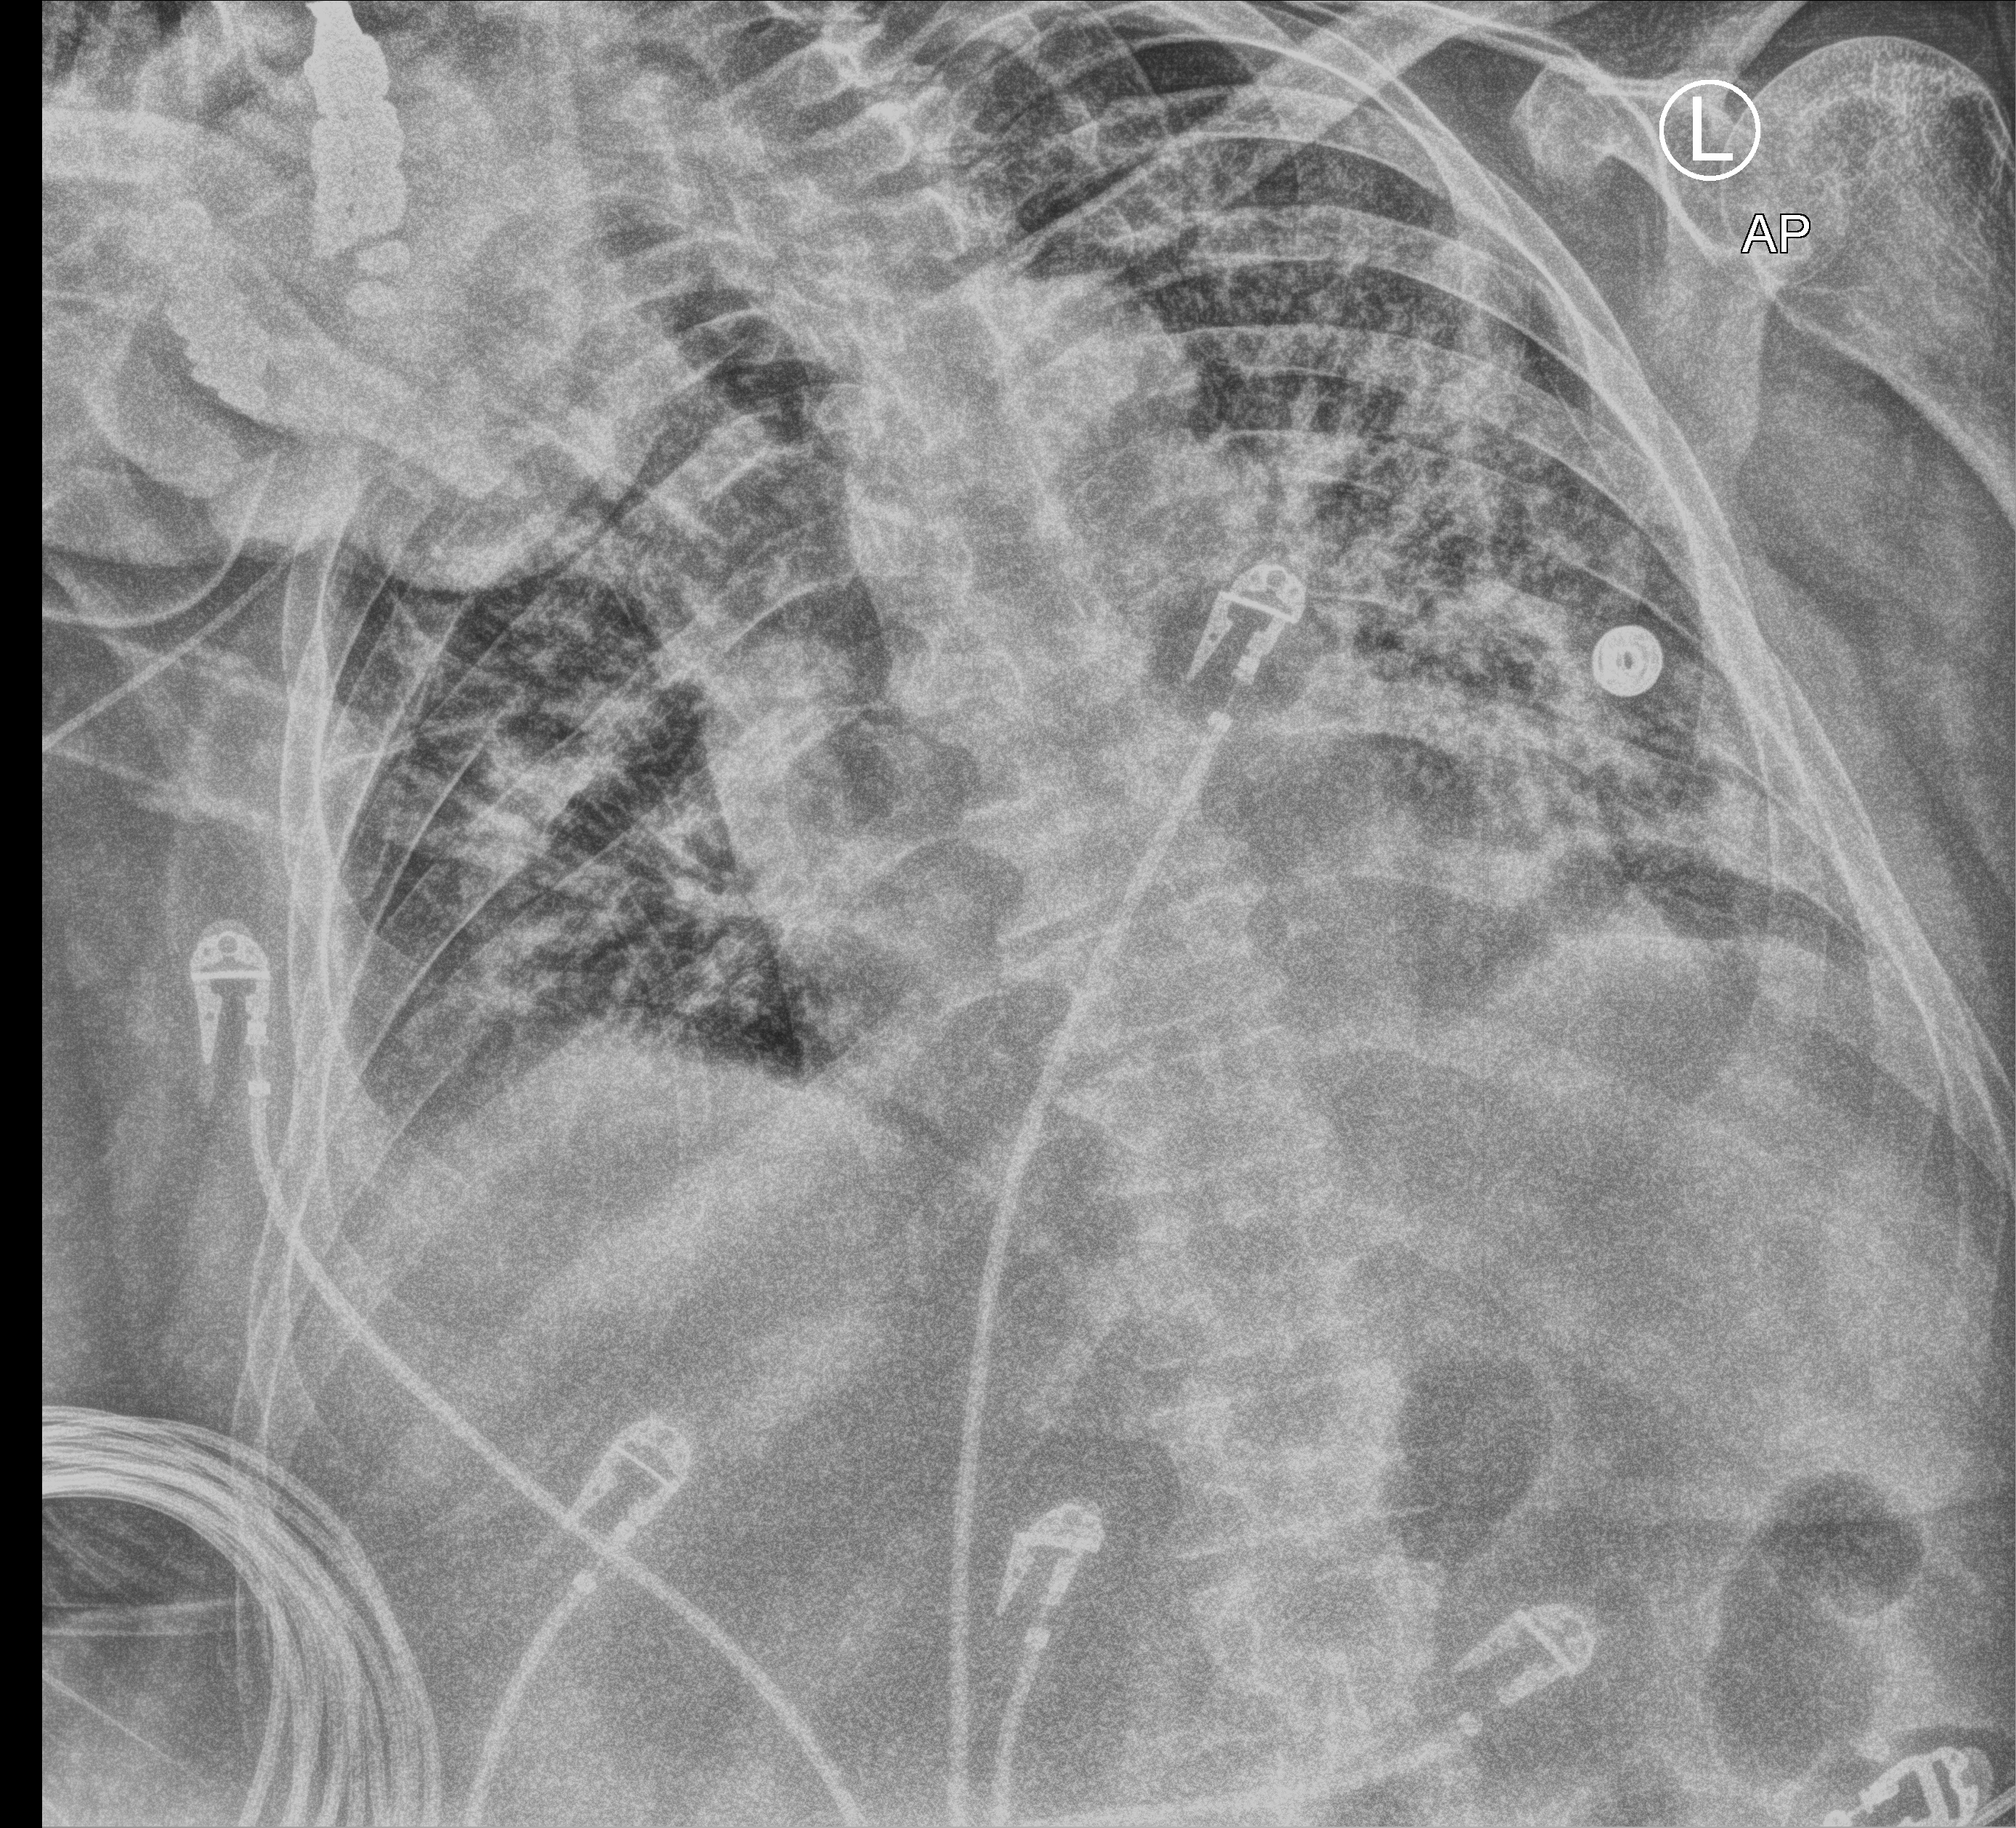
Chest X-ray (portable), anteroposterior (AP) projection. Male patient hospitalised with COVID-19, age 60–74 years.
Hospital-stay facts (about this admission, not read from this image; timing relative to this image not recorded): admitted to intensive care during this hospital stay: yes; smoking status (admission record): never; mechanically ventilated during this hospital stay: yes.